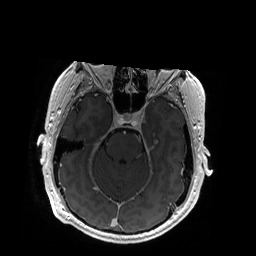
Brain MRI from a brain-tumour surgery series, one axial slice. Position 127 of 192 along the scan axis. T1-weighted post-contrast. 256 × 256 image matrix, field of view 256 × 256 mm. Case-level facts recorded for this patient, not image findings: histopathology: Glioblastoma; WHO grade: 4; IDH mutation: no.
Outlined on this slice (outlined manually by an expert reader):
- tumour: box from (x=155, y=141) to (x=158, y=144) px